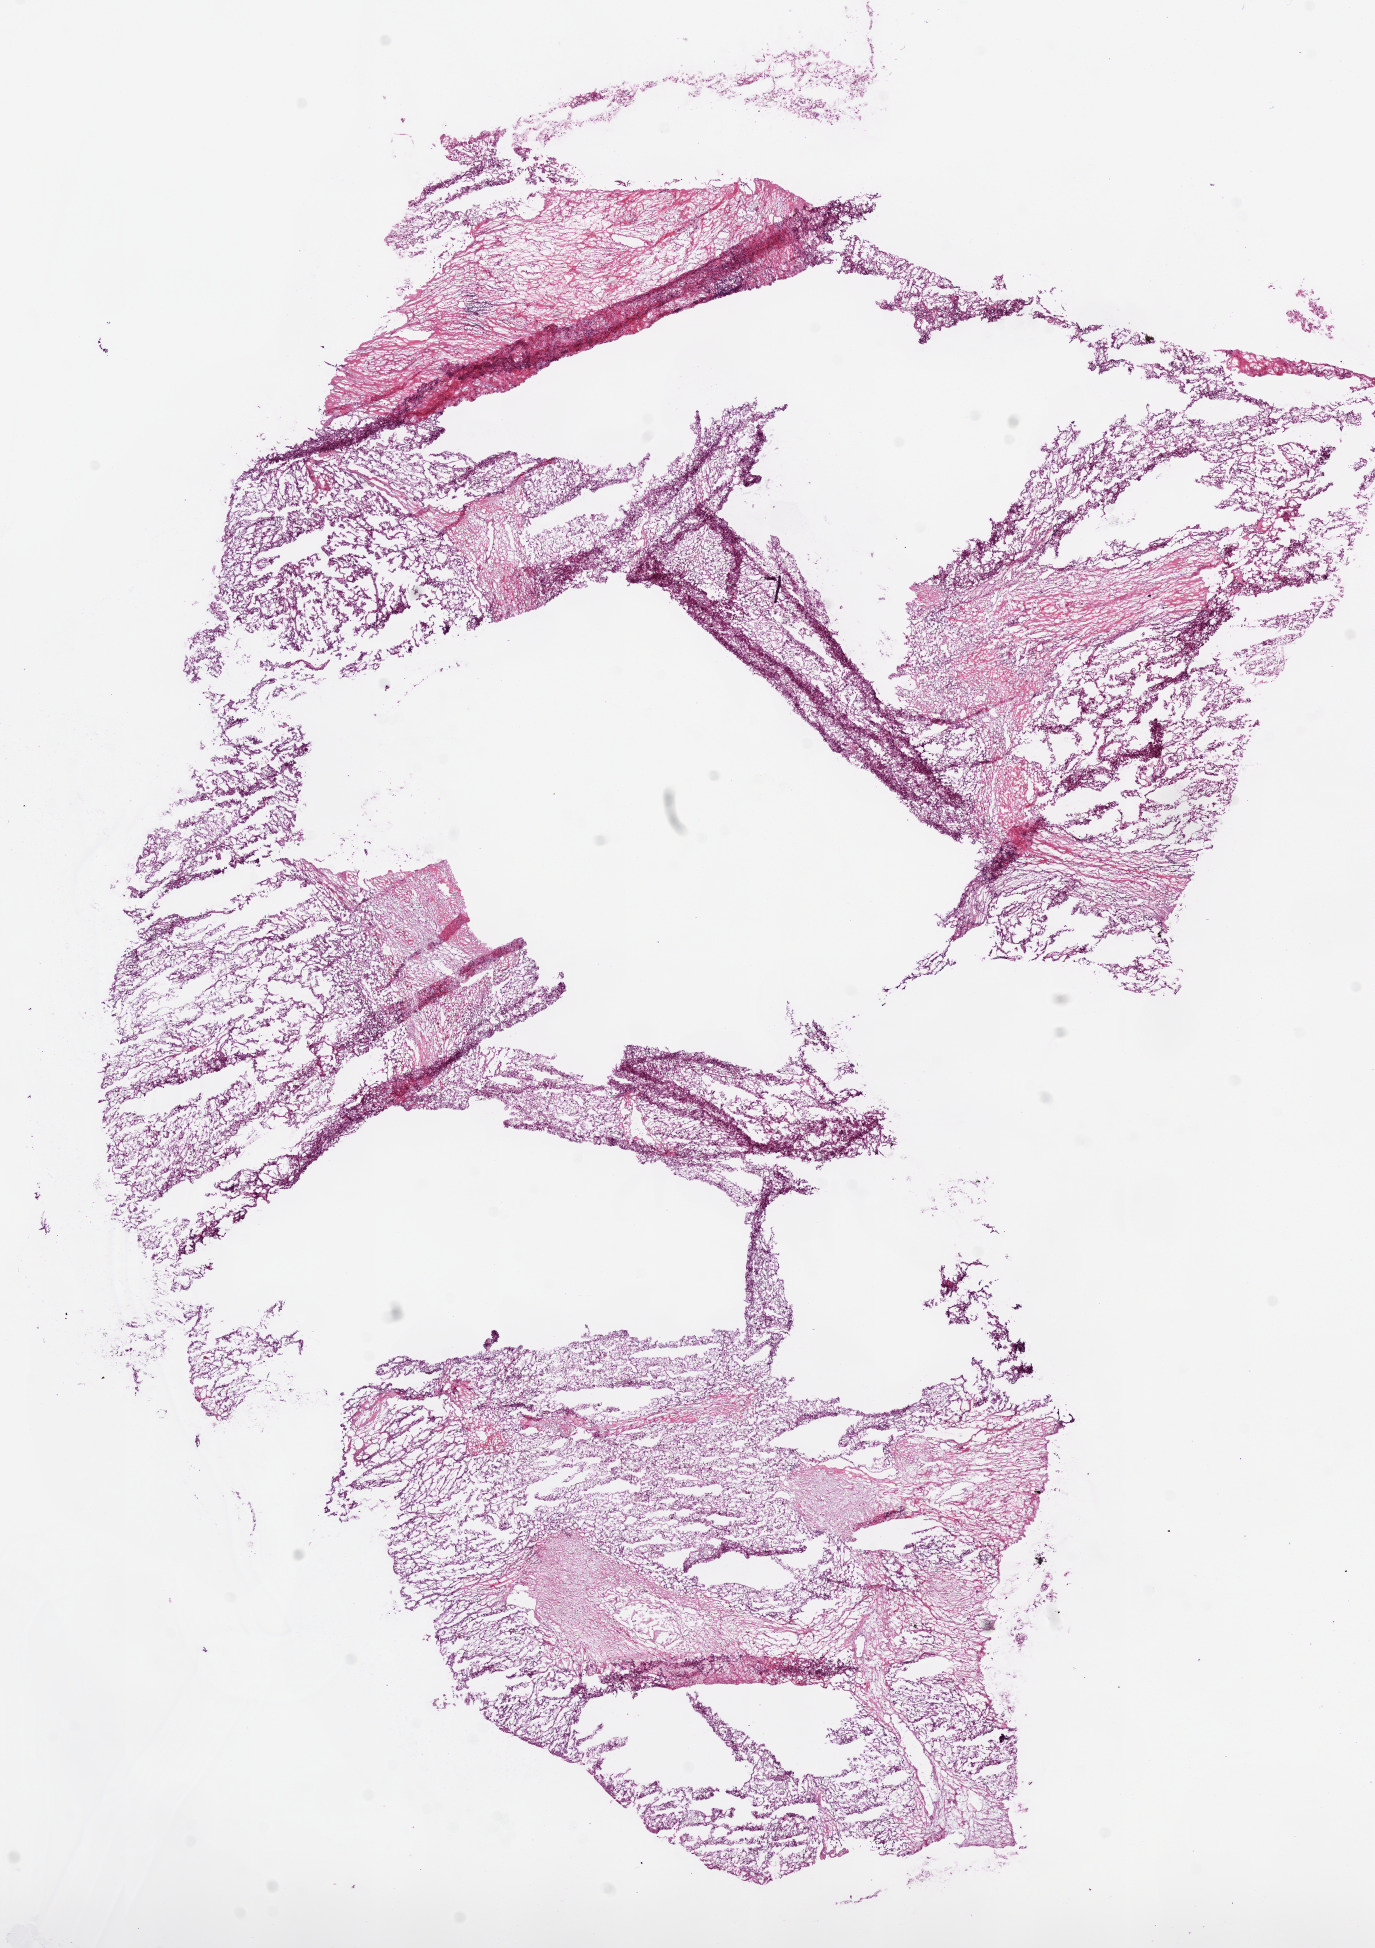
Digitized H&E-stained tissue section (whole slide) — a low-resolution overview of the entire scanned area, about 11.0 x 15.6 mm; frozen section from the bottom of the tissue portion; sample: primary tumour, kidney. Male, age 59 years at initial diagnosis. Histologic grade: G2 (moderately differentiated). Slide review estimates, as recorded: tumour cells 82%, tumour nuclei 85%, normal cells 0%, stromal cells 18%, necrosis 0%.
Laterality: right. AJCC pathologic stage: III. Diagnosis: Clear cell adenocarcinoma, NOS.